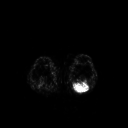
FDG PET of an extremity soft-tissue mass (from a PET/CT study), one axial slice; position 180 of 267 along the scan axis; 3.27 mm slice thickness; 128 × 128 image matrix, field of view 500 × 500 mm. Patient: male, 54 years. Case-level facts recorded for this patient, not image findings: histological type: synovial sarcoma; site of the primary tumour: left poplietal fossa.
Structures marked on this image (expert contour drawn on MRI and transferred to this co-registered scan by the dataset authors):
- gross tumour volume (mass): bounding box <73,81,90,92> (left, top, right, bottom; pixels)